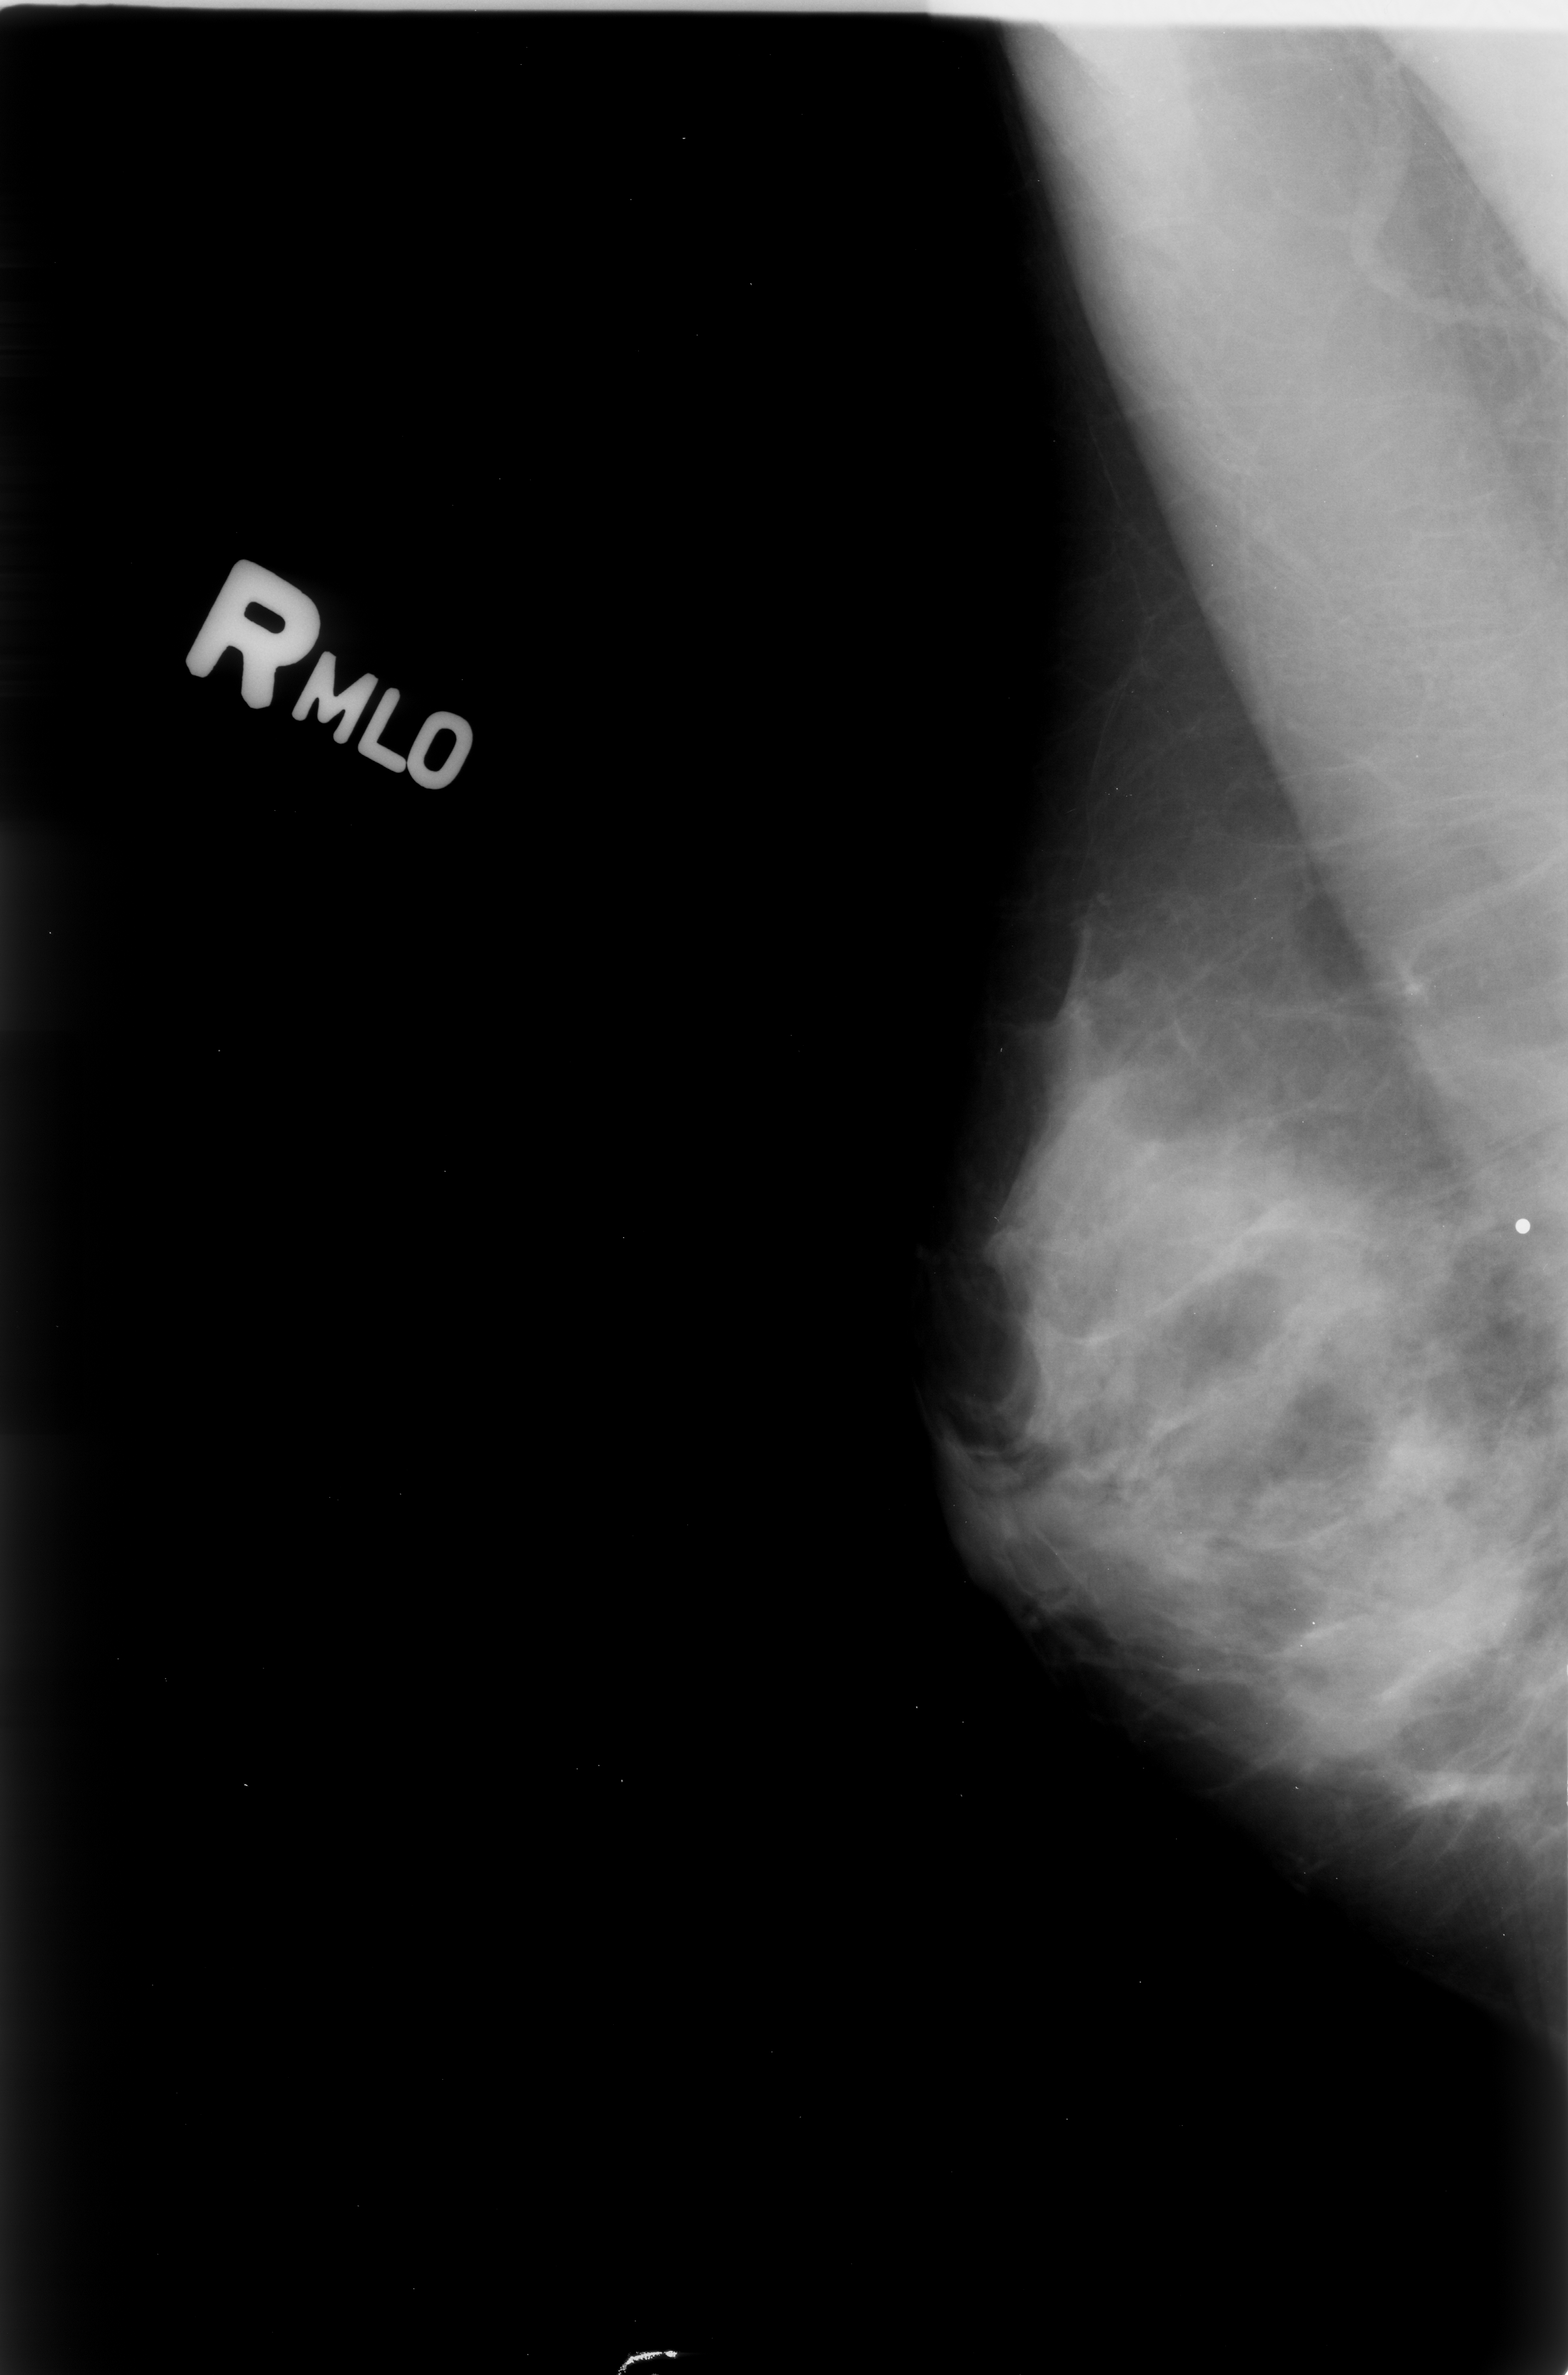
Mammogram (digitized film). Right breast. Mediolateral oblique (MLO) view. BI-RADS breast density category 4 (scale 1–4). 1568 × 2375 image matrix.
Expert-marked regions of interest on this film, with their recorded descriptors:
- calcifications, morphology pleomorphic, distribution clustered; BI-RADS assessment category 4; subtlety rating 2 on a 1 (subtle) to 5 (obvious) scale; pathology result (as recorded, not read from the image): benign: box from (x=1271, y=1283) to (x=1381, y=1398) px